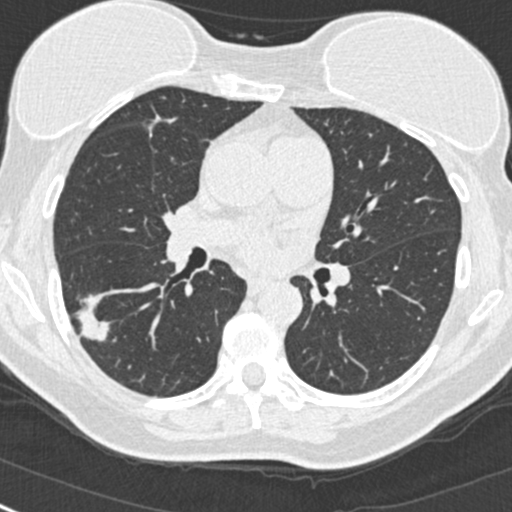
Low-dose screening chest CT, one axial slice. Slice 143 of 268 in the series (ordered by position). Reconstruction kernel B30f. Lung window (W 1500 / L -600 HU). 1 mm slice thickness. 512 × 512 image matrix, field of view 296 × 296 mm.
Annotated regions visible in this slice (outlined manually by an expert reader):
- lesion 1 (tumor, upper lobe of right lung): bounding box <77,295,109,341> (left, top, right, bottom; pixels)